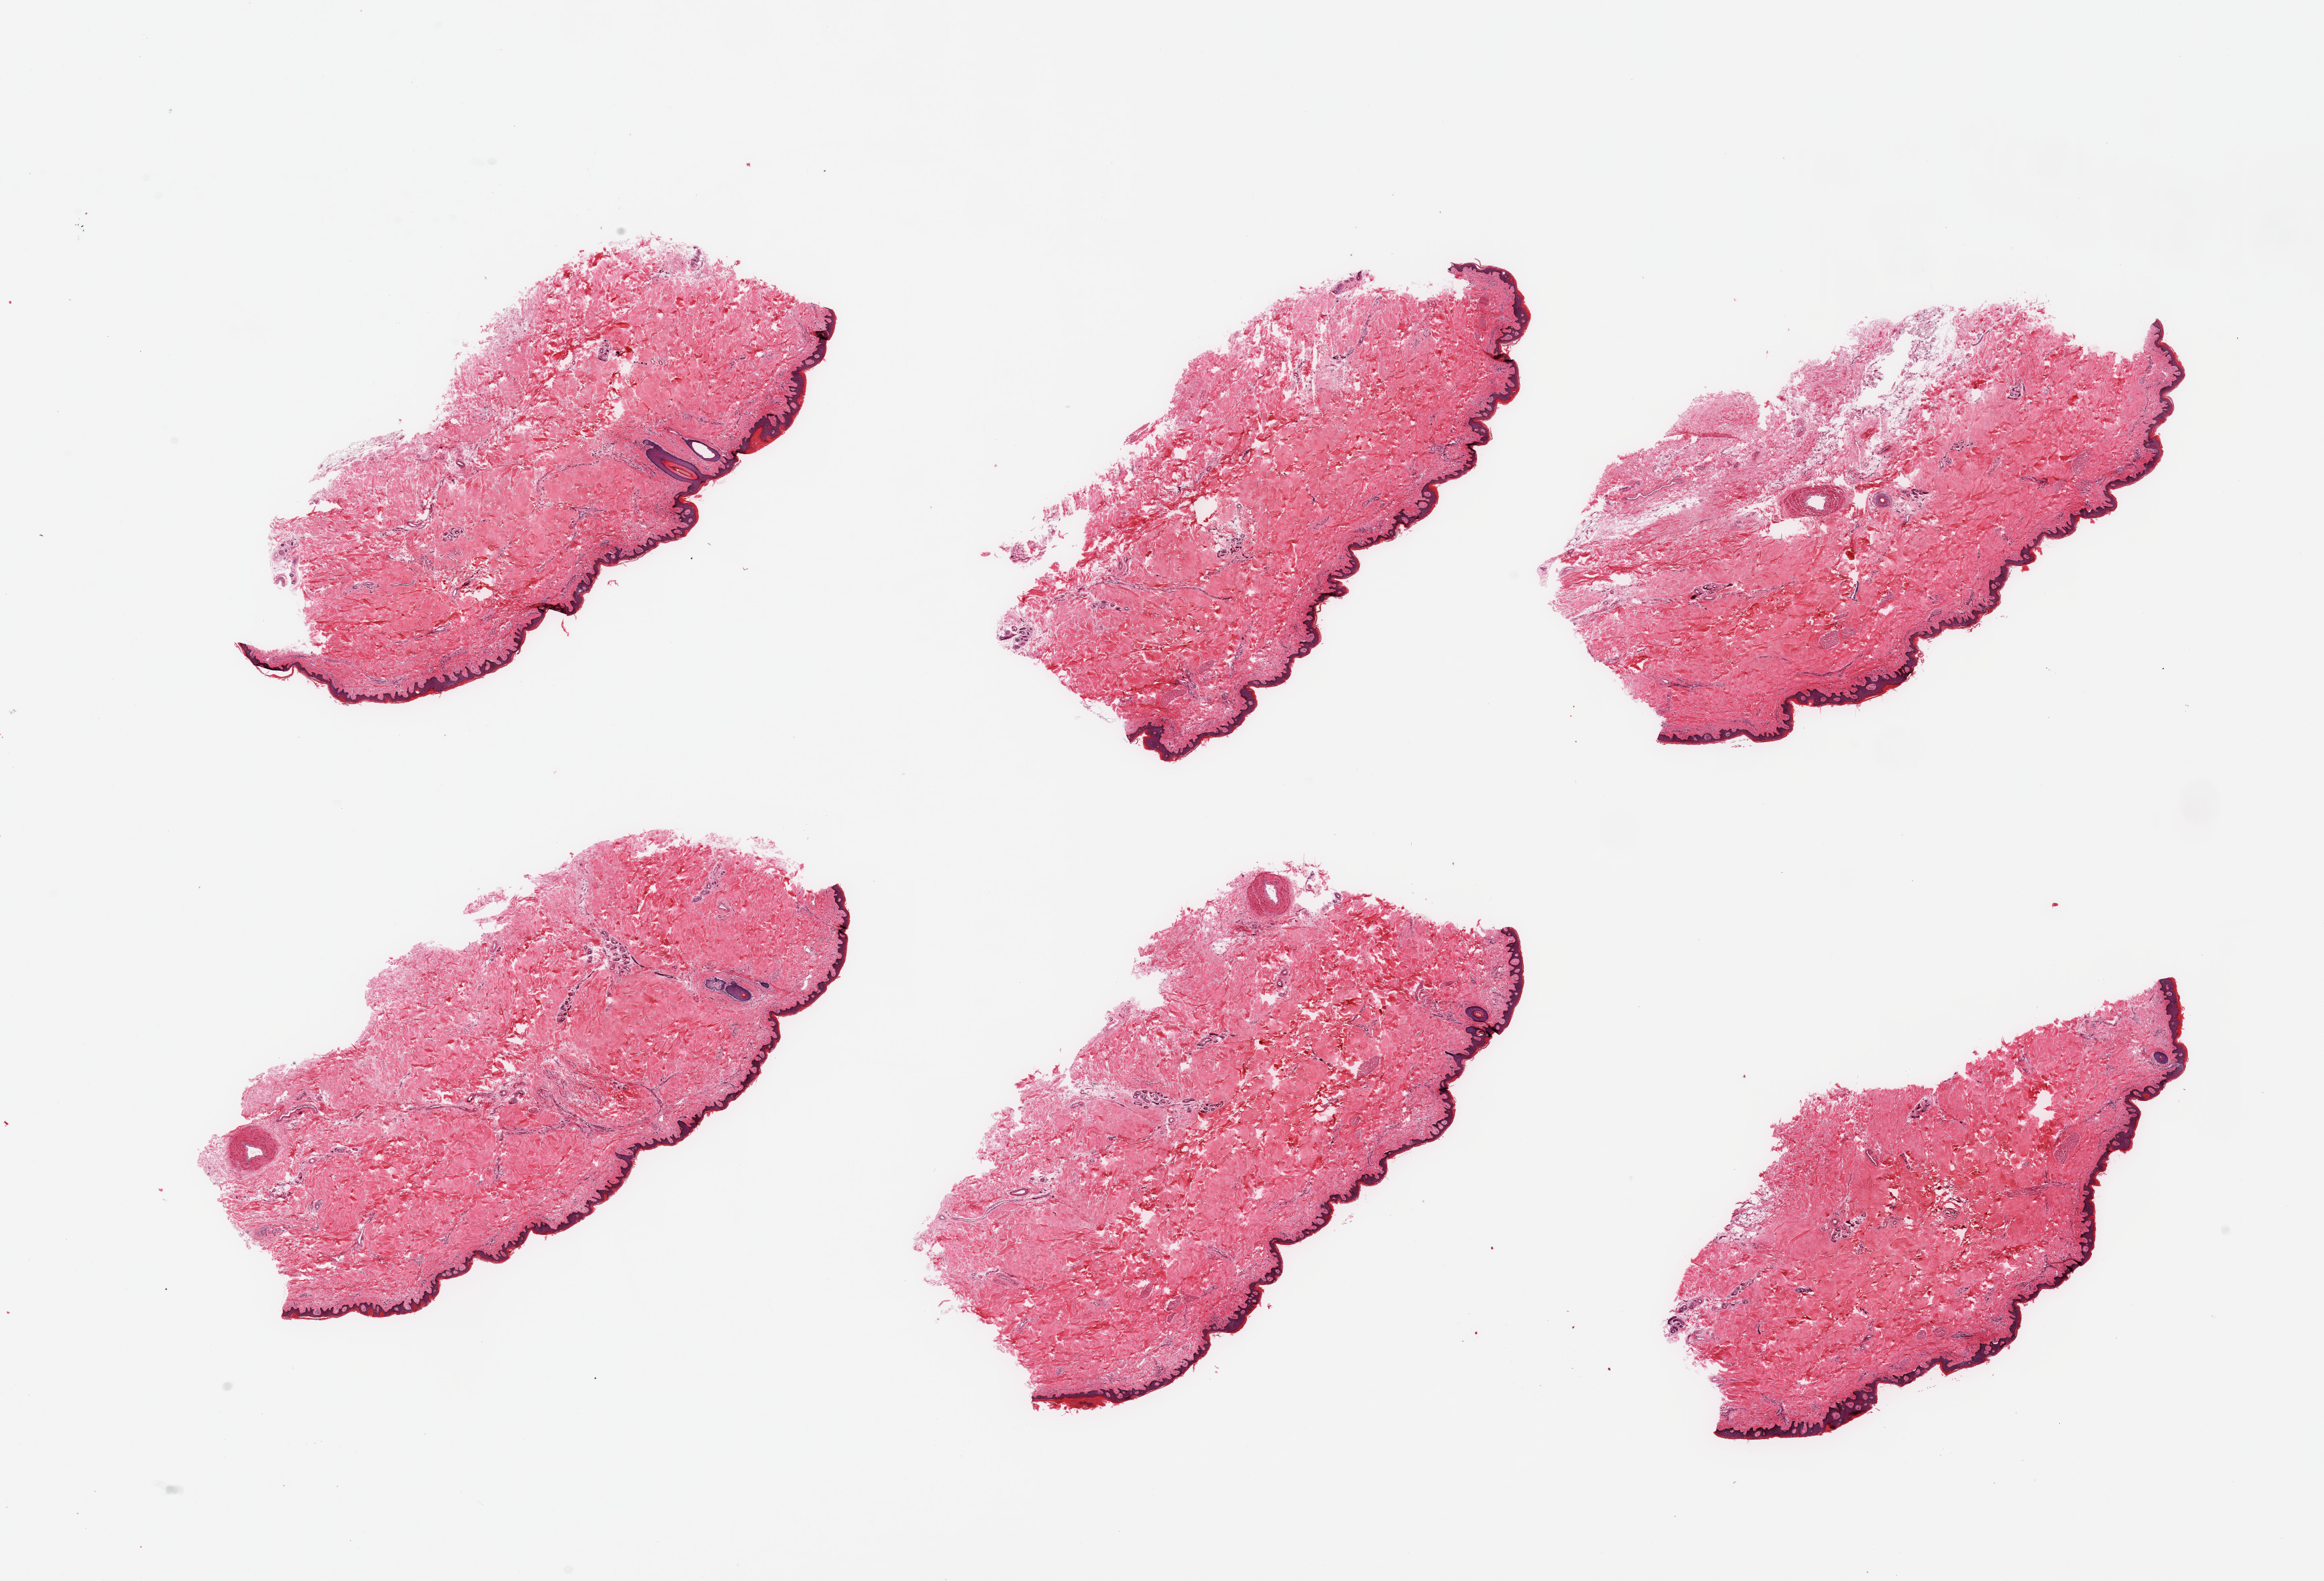
Hematoxylin and eosin (H&E) whole-slide image, brightfield — low-resolution overview of the scanned area, about 27.6 x 18.8 mm. PAXgene-fixed, paraffin-embedded tissue. Section of skin of lower leg (target tissue). Tissue donor sample. Donor: male.
Reviewer comment on this tissue sample: 6 pieces; ~47um thick epidermis; essentially well trimmed except one piece containing ~15% external fat.